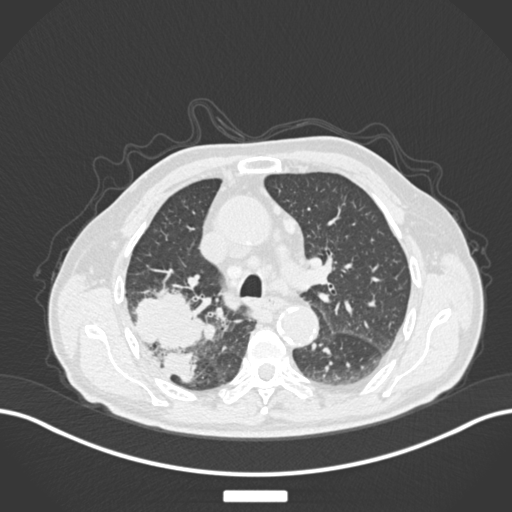
Chest CT, one axial slice; slice 123 of 201 in the series (ordered by position); lung window (W 1500 / L -600 HU); 1 mm slice thickness; 512 × 512 image matrix, field of view 400 × 400 mm. Patient: male, 72 years. From the clinical record (not read from this slice): clinical TNM (as recorded): T3 N2 M0.
Outlined on this slice (bounding box drawn by a radiologist):
- lung tumour (recorded histology: adenocarcinoma): bounding box <130,283,209,384> (left, top, right, bottom; pixels)